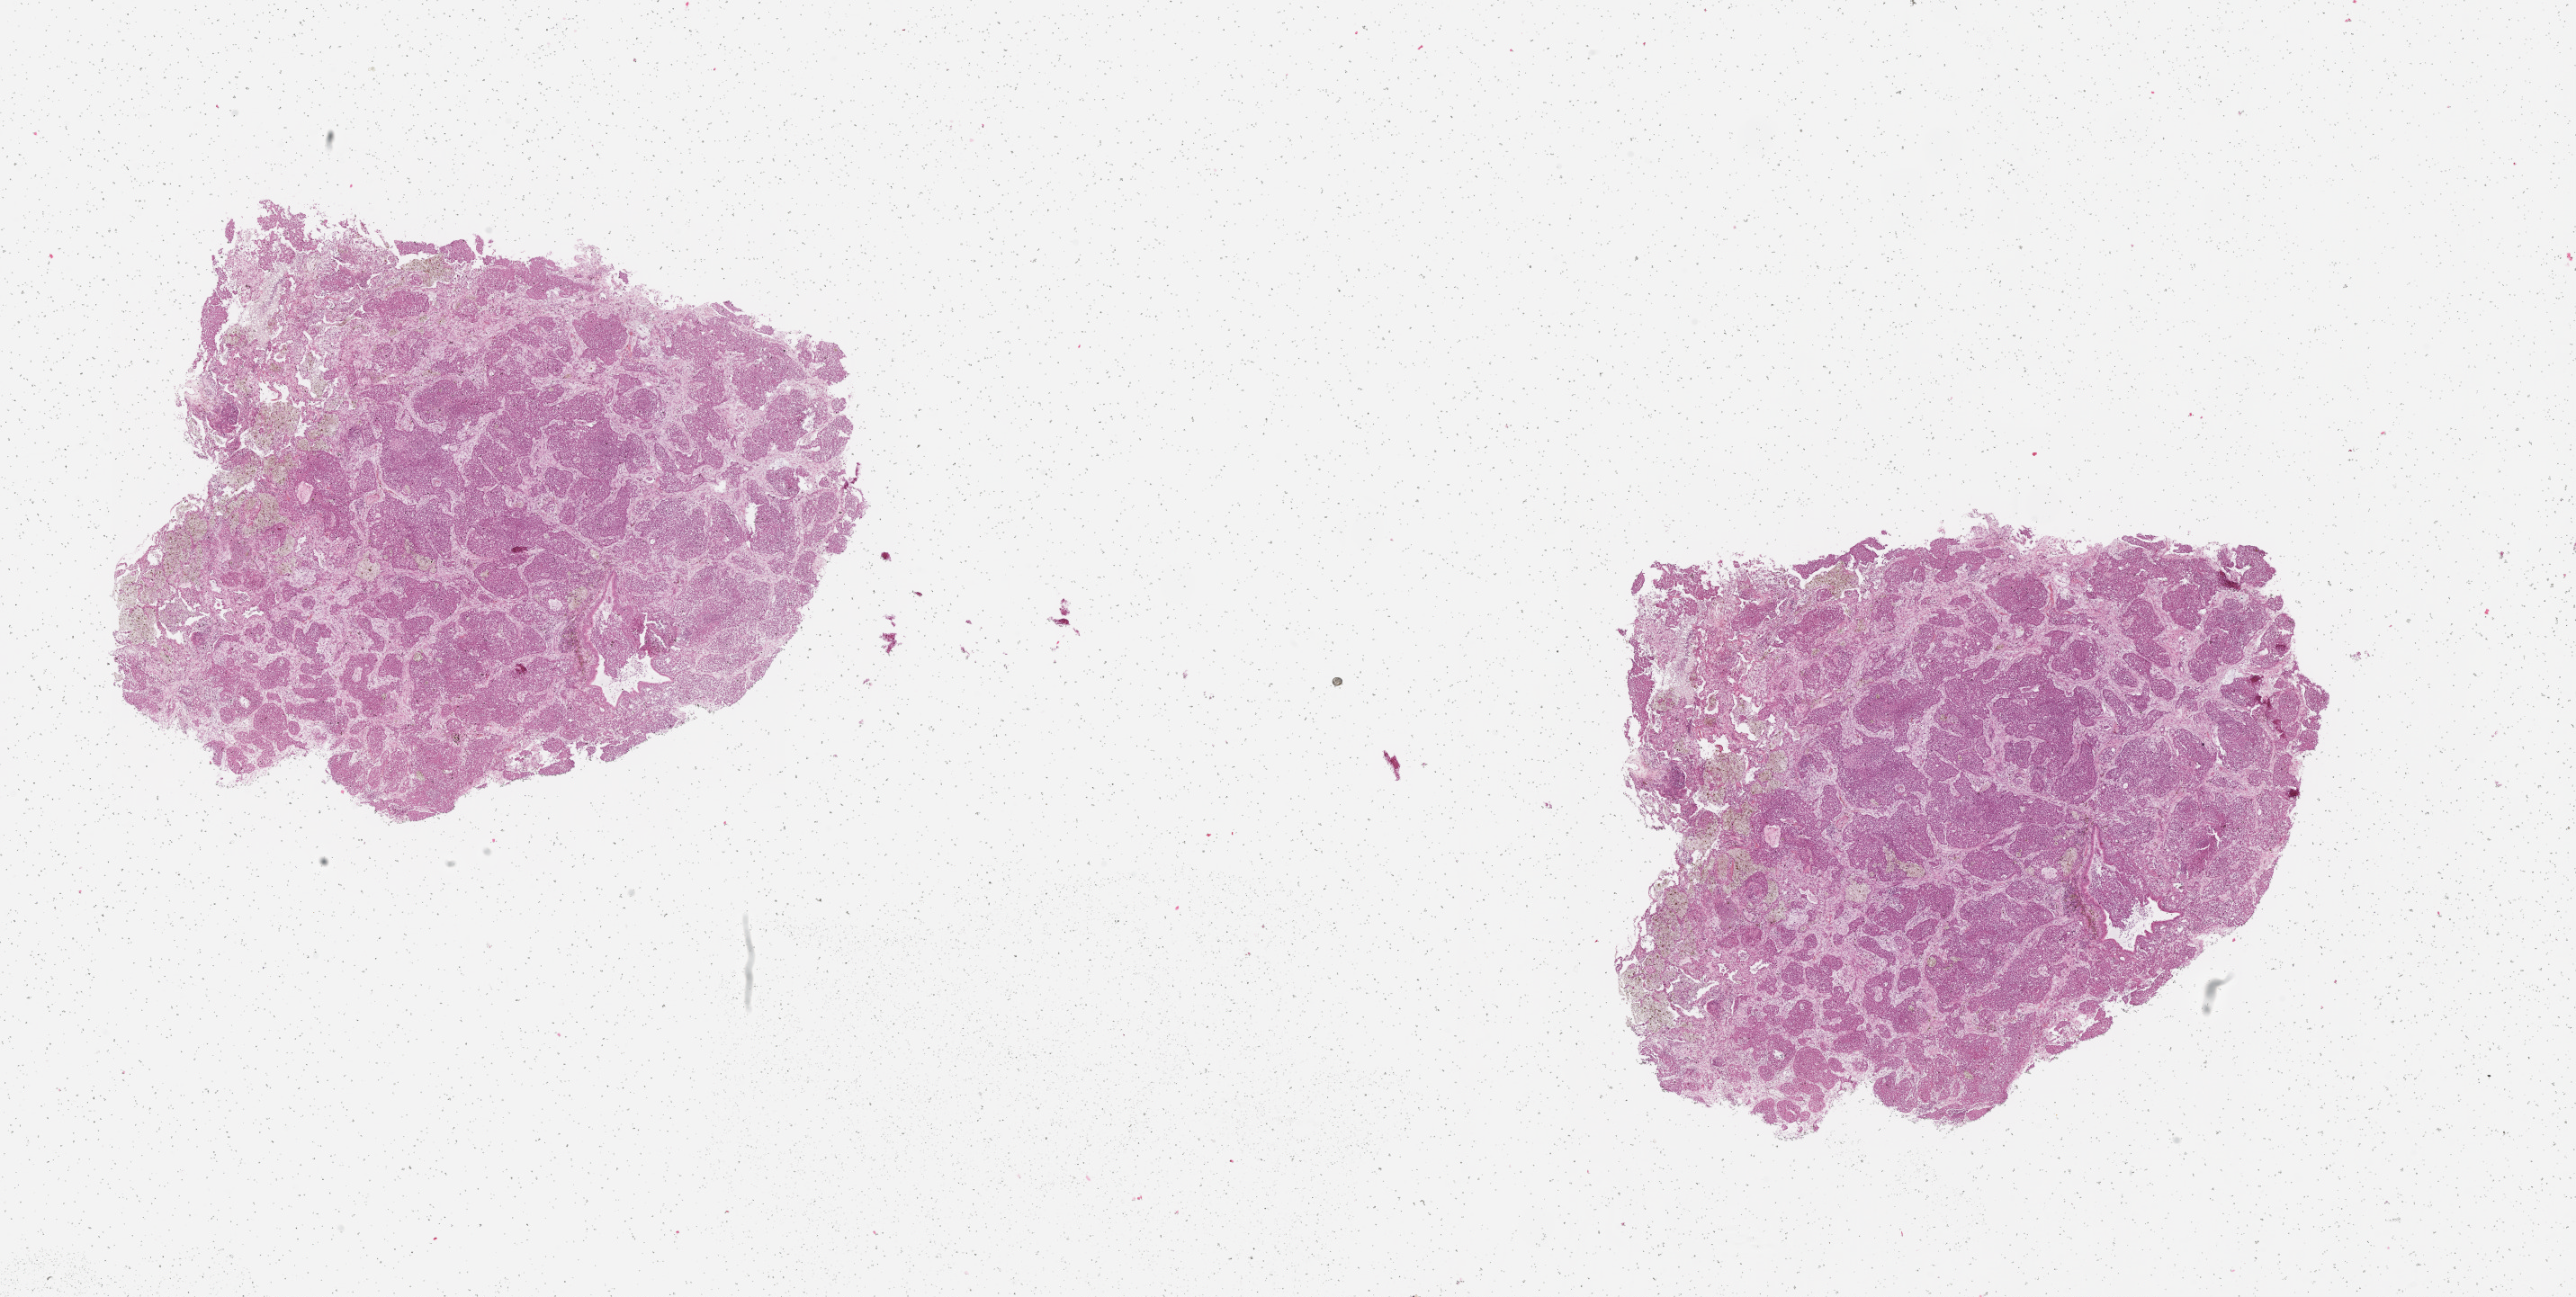
Whole-slide histology image, Hematoxylin and eosin (H&E) stained — low-resolution overview of the scanned area, about 23.1 x 11.6 mm (from a 20x scan), tumour tissue sample, sampled site: lung. Patient: female, age 70 years. Composition of this section per pathologist review: tumour nuclei 80%, necrosis 5%.
Diagnosis: Adenocarcinoma, NOS.